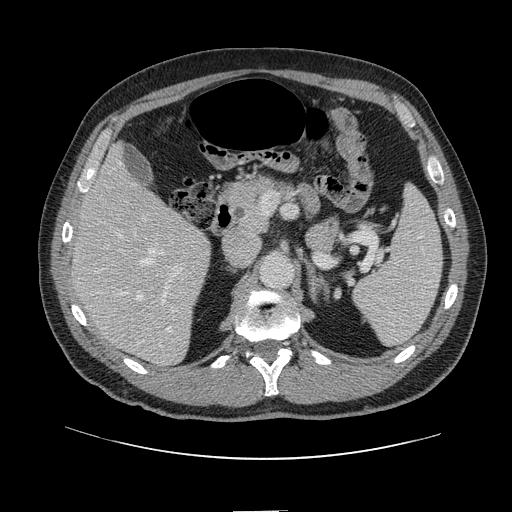
Contrast-enhanced abdominal CT, one axial slice; slice 71 of 161 in the series (ordered by position); 120 kVp; intravenous contrast given; soft-tissue window (W 400 / L 40 HU); 512 × 512 image matrix, field of view 412 × 412 mm. Male patient, age 66 years. Case-level facts recorded for this patient, not image findings: diagnosis: colorectal cancer liver metastases, imaged before liver resection; multiple liver metastases: no; largest metastasis: 3.5 cm; disease in both lobes: no.
Annotated regions visible in this slice (outlined manually by an expert reader):
- hepatic veins: bounding box <118,162,174,332> (left, top, right, bottom; pixels)
- liver: <73,150,210,365>
- planned liver remnant (the part of the liver to remain after resection): <72,149,188,292>
- portal vein (with intrahepatic branches): <119,215,184,305>